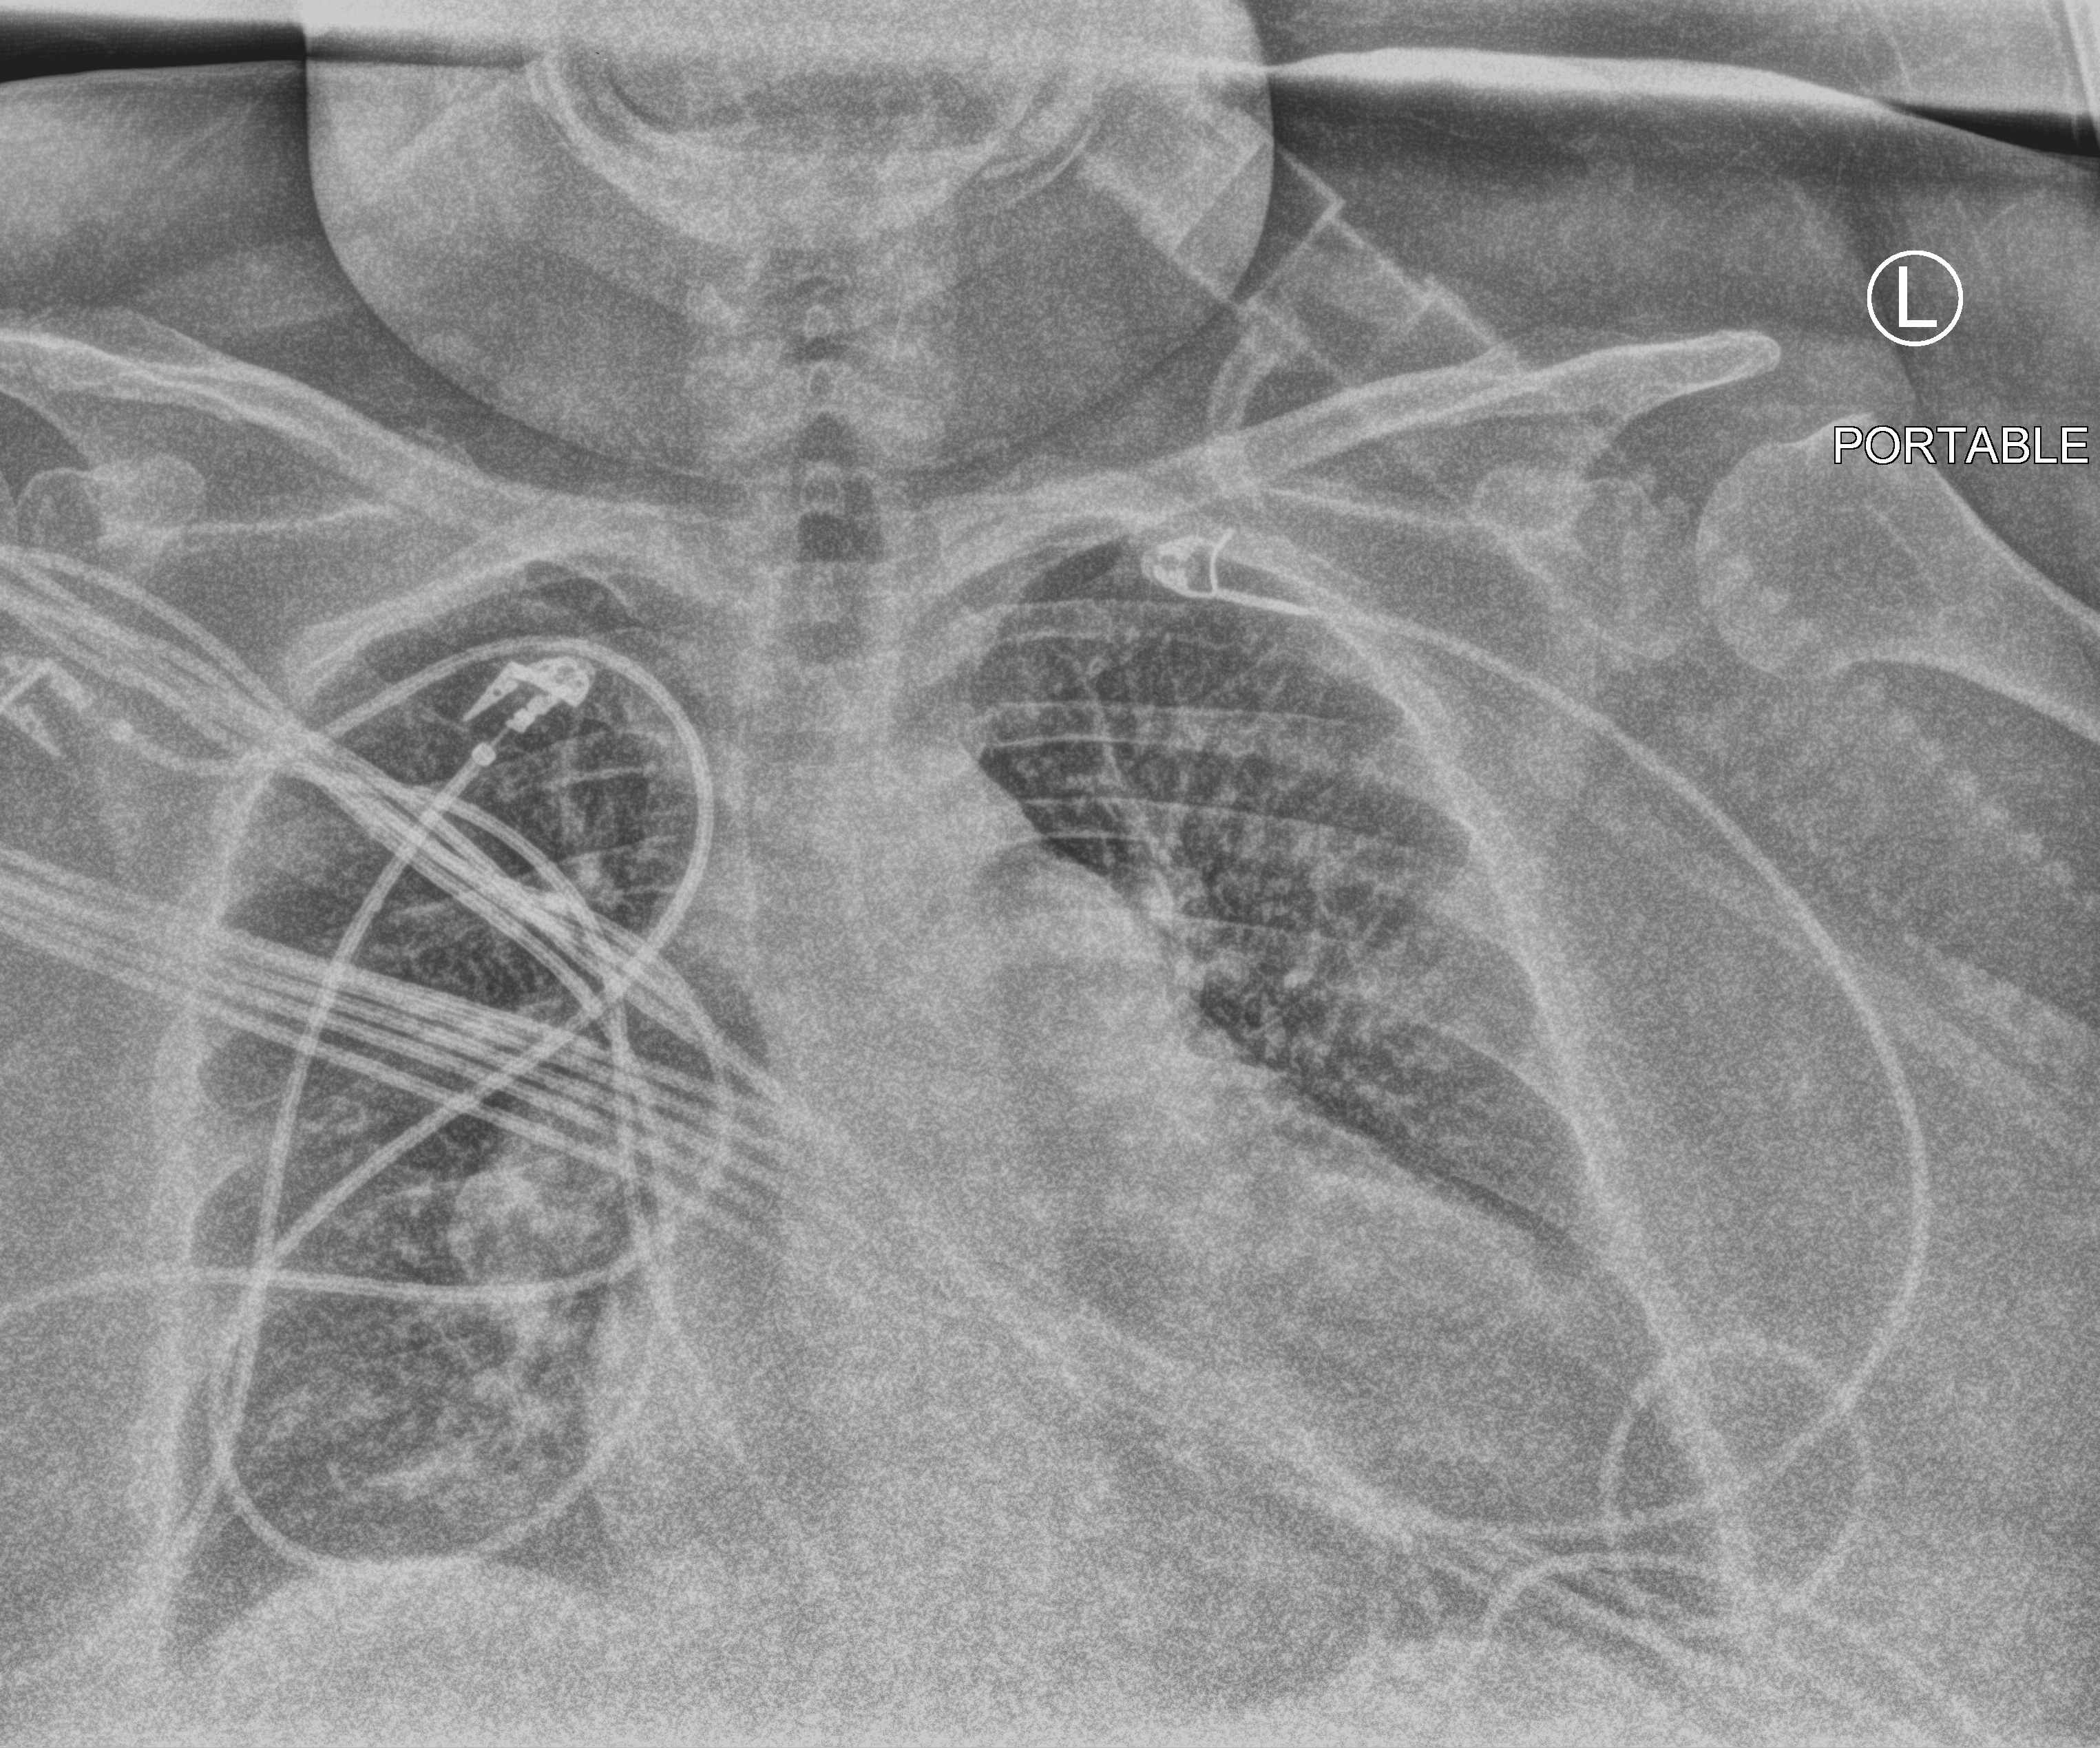
Chest X-ray (portable), anteroposterior (AP) projection. Patient hospitalised with COVID-19; female, aged 60–74 years.
From the hospital-stay record, not from the radiograph (when in the stay this image was taken is not recorded): mechanically ventilated during this hospital stay: yes; length of hospital stay: 6 days; COPD (admission record): yes.